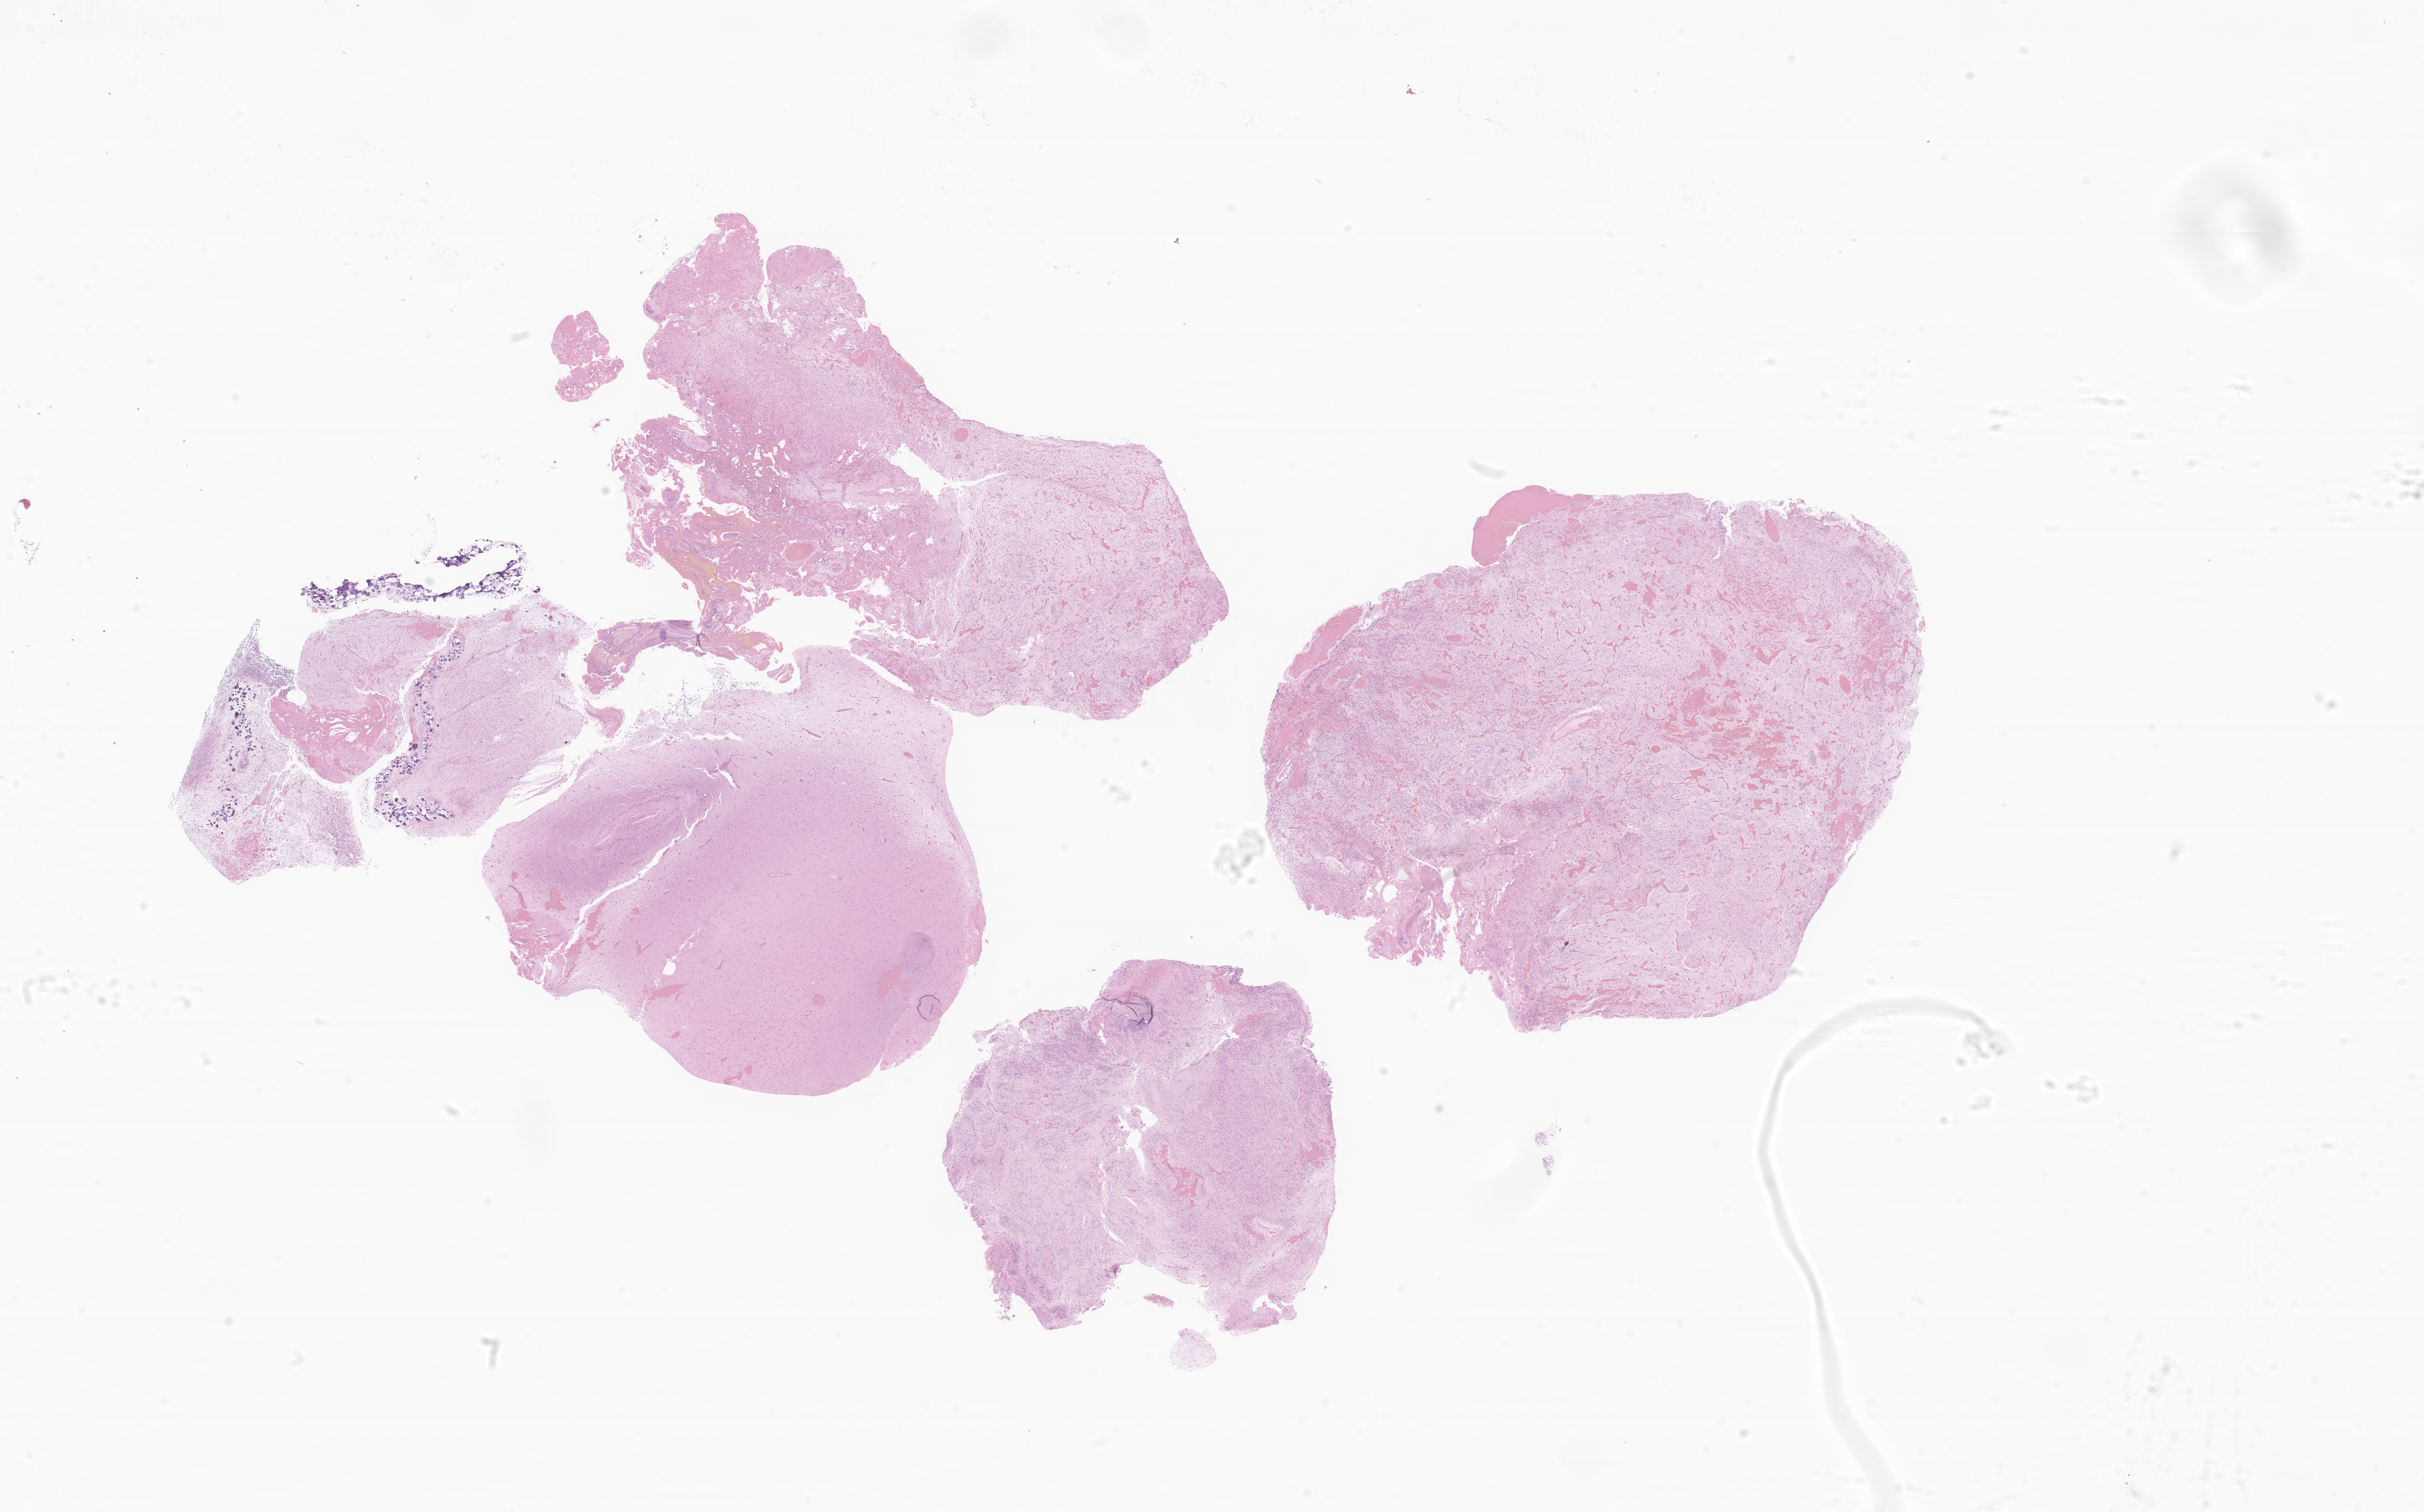
Haematoxylin and eosin whole-slide image of tumor tissue from the brain, a low-resolution overview of the entire scanned area, about 26.3 x 16.4 mm; formalin-fixed, paraffin-embedded (FFPE) tissue. Male patient, age 191 months (15 years 11 months).
• diagnosis: Neoplasm, malignant